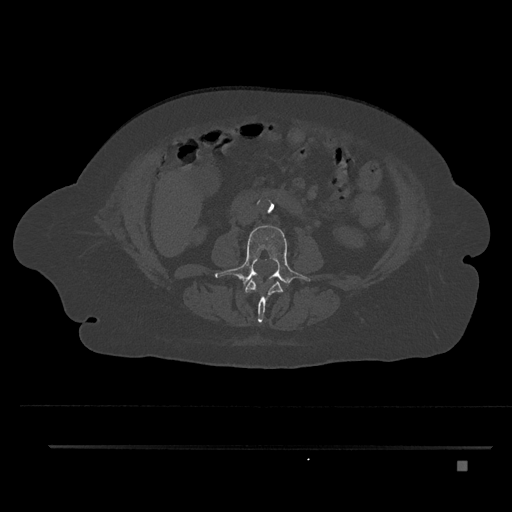
CT including the spine, one axial slice; 120 kVp; bone window (W 1800 / L 400 HU); 0.5 mm slice thickness; 512 × 512 image matrix. Patient: female, 76 years. Case-level facts recorded for this patient, not image findings: primary cancer: lung; vertebrae with lytic lesions (as recorded): T11, L3.
Structures marked on this image (semi-automatically segmented with operator editing):
- L2 vertebra: bounding box (x1, y1, x2, y2) in pixels: (245, 278, 283, 323)
- L3 vertebra: (215, 225, 310, 289)